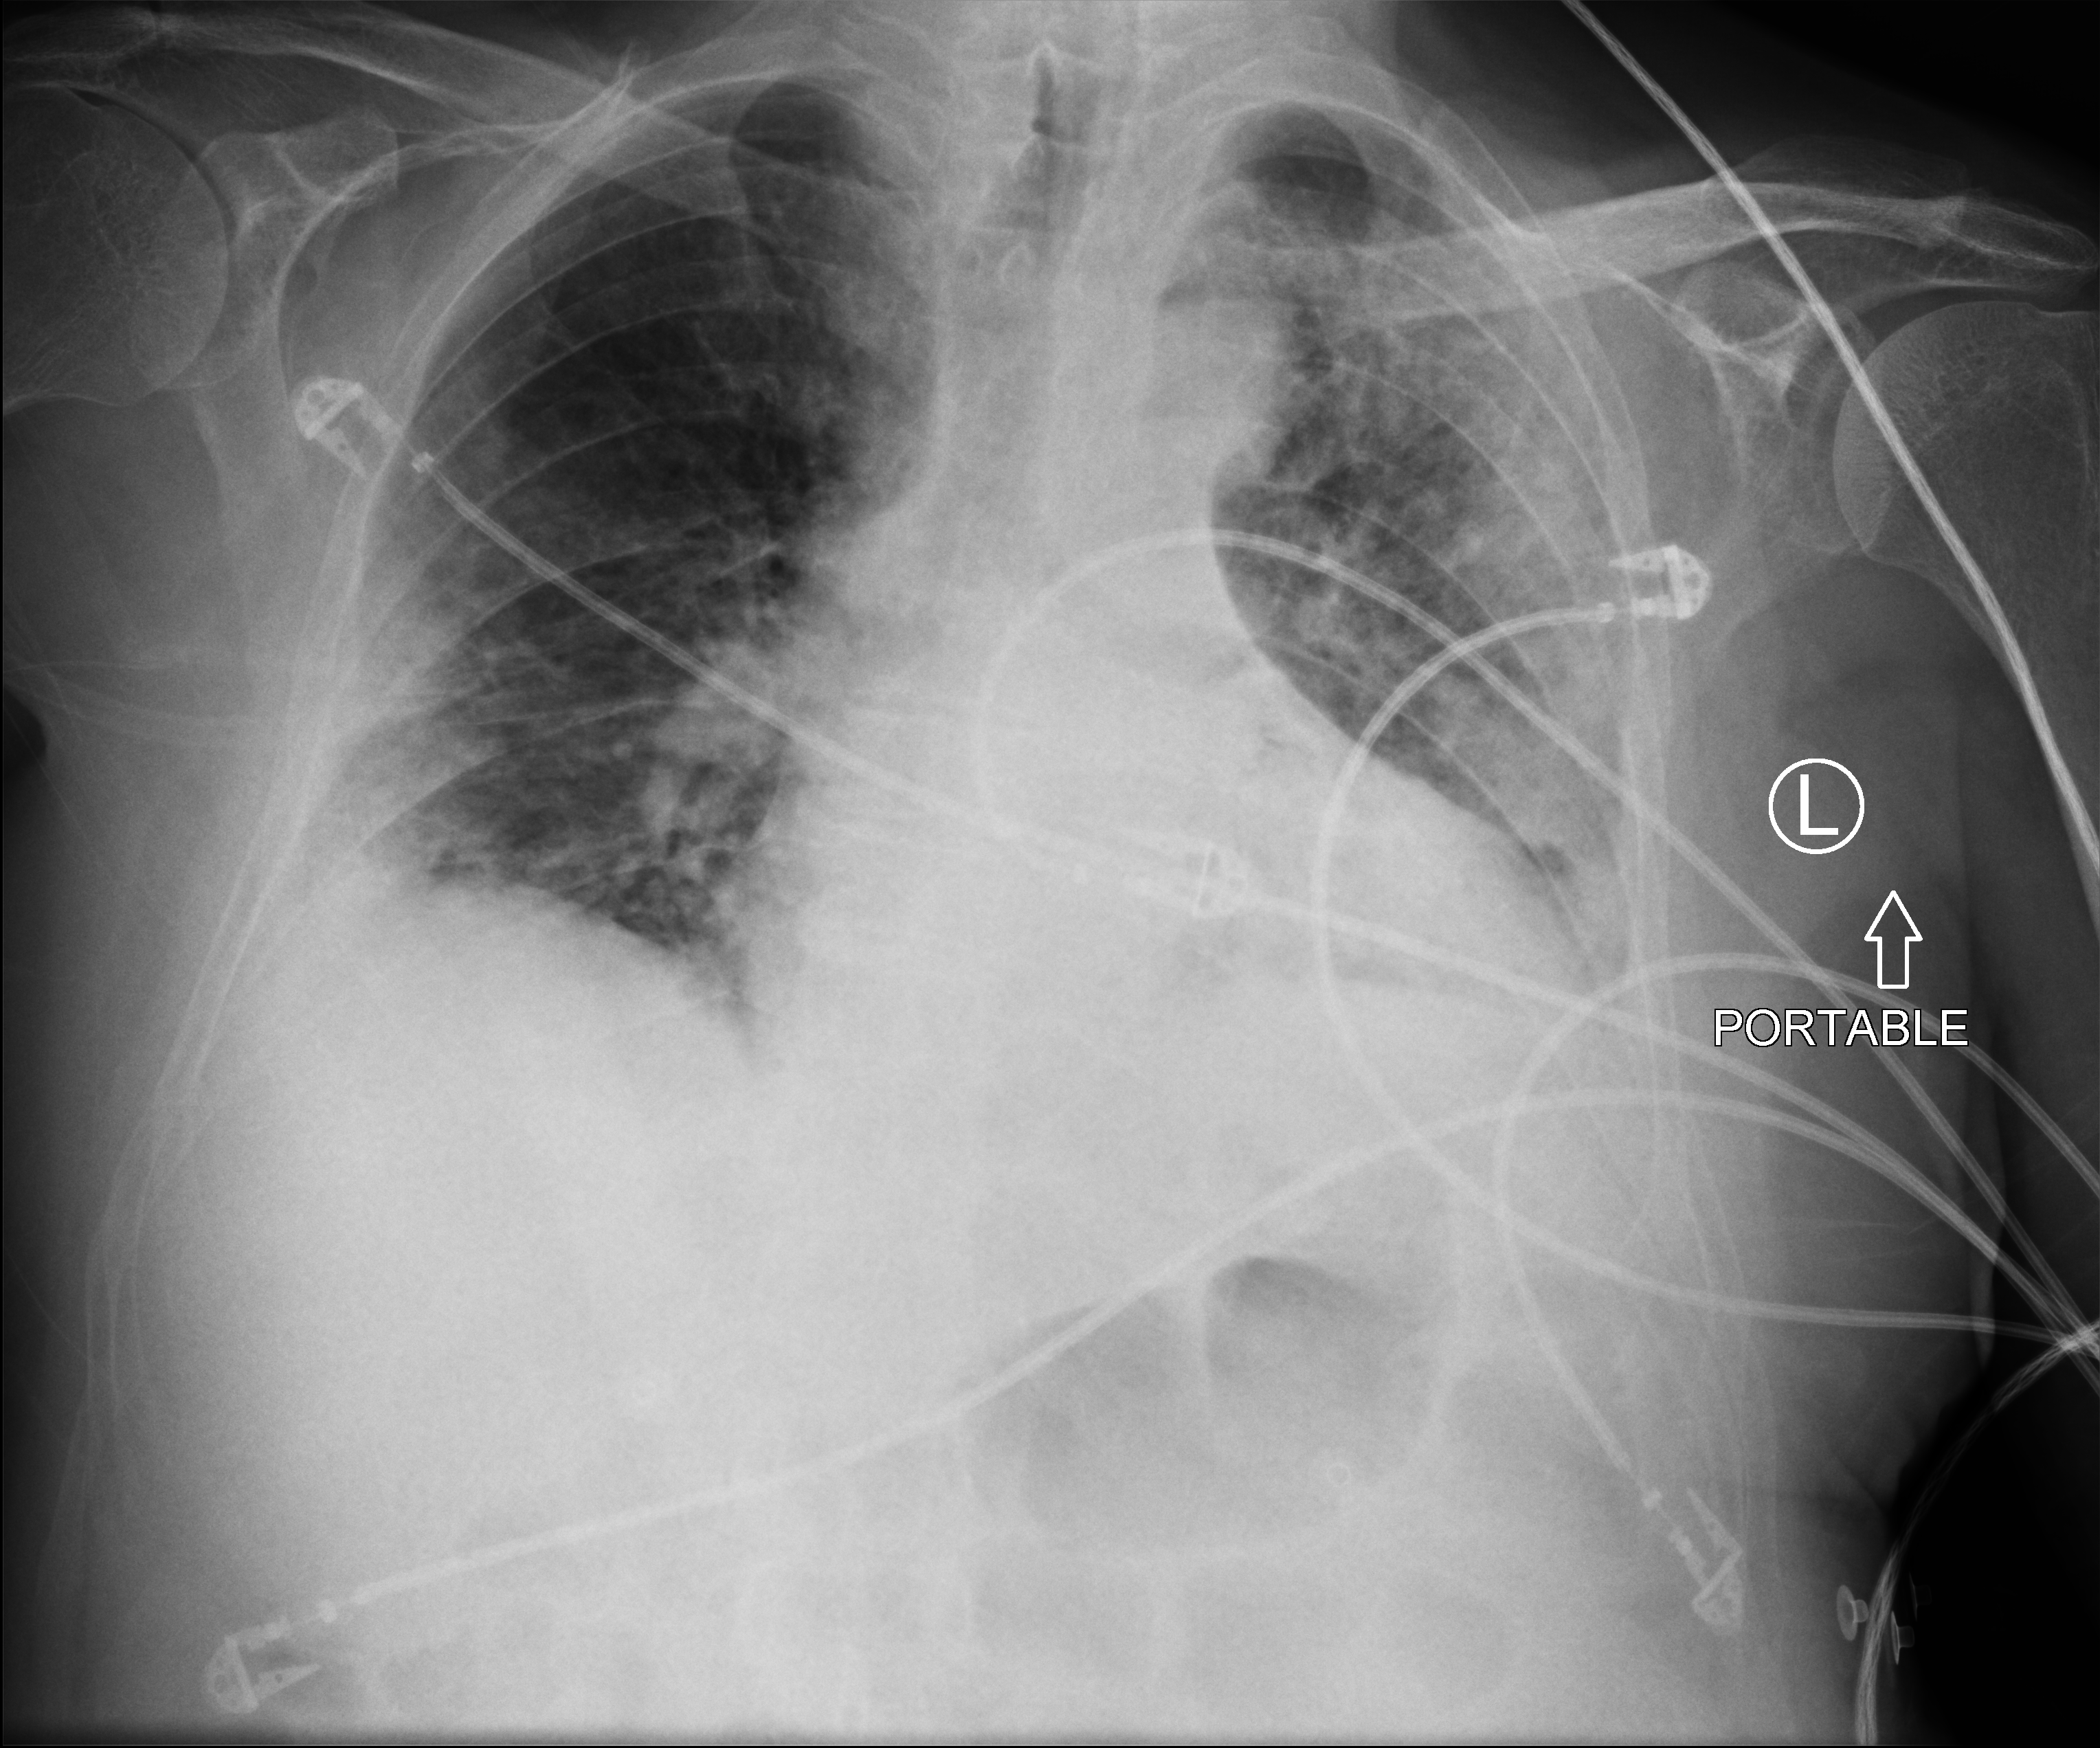
Portable chest radiograph. Male patient hospitalised with COVID-19, age 60–74 years.
Hospital-stay facts (about this admission, not read from this image; timing relative to this image not recorded): admitted to intensive care during this hospital stay: no; length of hospital stay: 9 days; mechanically ventilated during this hospital stay: no.